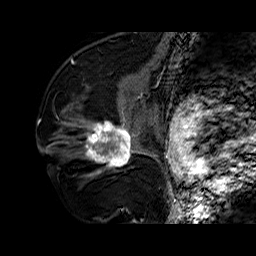
Breast MRI (dynamic contrast-enhanced), one sagittal slice. Position 36 of 60 along the scan axis. Dynamic contrast-enhanced series, time point 2 of 6 at this slice position (early post-contrast). 1.5 T. TE 6.4 ms, TR 32.7 ms. 4 mm slice thickness. 256 × 256 image matrix. Female patient. Case-level facts recorded for this patient, not image findings: setting: breast cancer imaged before/during neoadjuvant chemotherapy; receptor status: HR-positive, HER2-negative.
Annotated regions visible in this slice (semi-automatically segmented with operator editing):
- analysis volume of interest (the breast-tissue region the enhancement analysis was run in; not a lesion): box from (x=73, y=110) to (x=141, y=179) px
- tumour enhancement mask (voxels above the 100 % enhancement threshold inside the analysis volume of interest): (x=86, y=123)–(x=136, y=167)